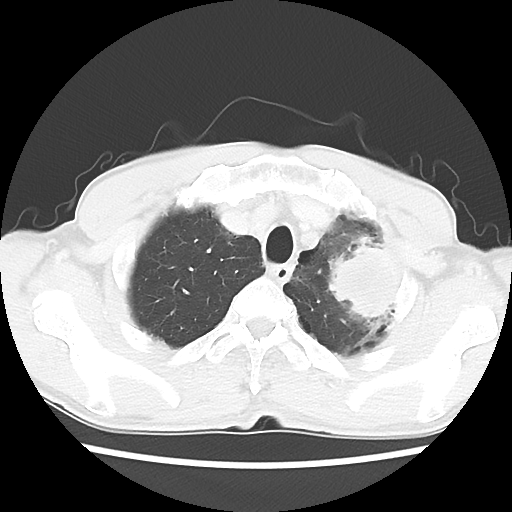
Chest CT, one axial slice; slice 51 of 60 in the series (ordered by position); reconstruction kernel LUNG; lung window (W 1500 / L -600 HU); 512 × 512 image matrix. Patient: male, 64 years. From the clinical record (not read from this slice): clinical TNM (as recorded): T3 N3 M0.
Structures marked on this image (bounding box drawn by a radiologist):
- lung tumour (recorded histology: adenocarcinoma): bounding box (x1, y1, x2, y2) in pixels: (322, 231, 431, 334)